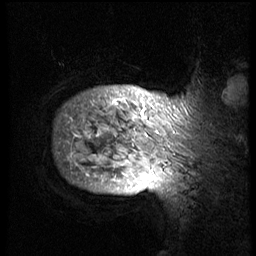
Breast MRI (dynamic contrast-enhanced), one sagittal slice. Position 66 of 74 along the scan axis. 3 images stored at this slice position (order not interpretable as contrast timing). 1.5 T. TE 4.2 ms, TR 8.9 ms. 2.5 mm slice thickness. 256 × 256 image matrix. Patient: female, 57 years. Case-level facts recorded for this patient, not image findings: setting: breast cancer imaged before/during neoadjuvant chemotherapy; receptor status: HER2-positive.
Outlined on this slice (semi-automatically segmented with operator editing):
- analysis volume of interest (the breast-tissue region the enhancement analysis was run in; not a lesion): bounding box (x1, y1, x2, y2) in pixels: (46, 62, 242, 175)
- tumour enhancement mask (voxels above the 140 % enhancement threshold inside the analysis volume of interest): (71, 94, 186, 175)